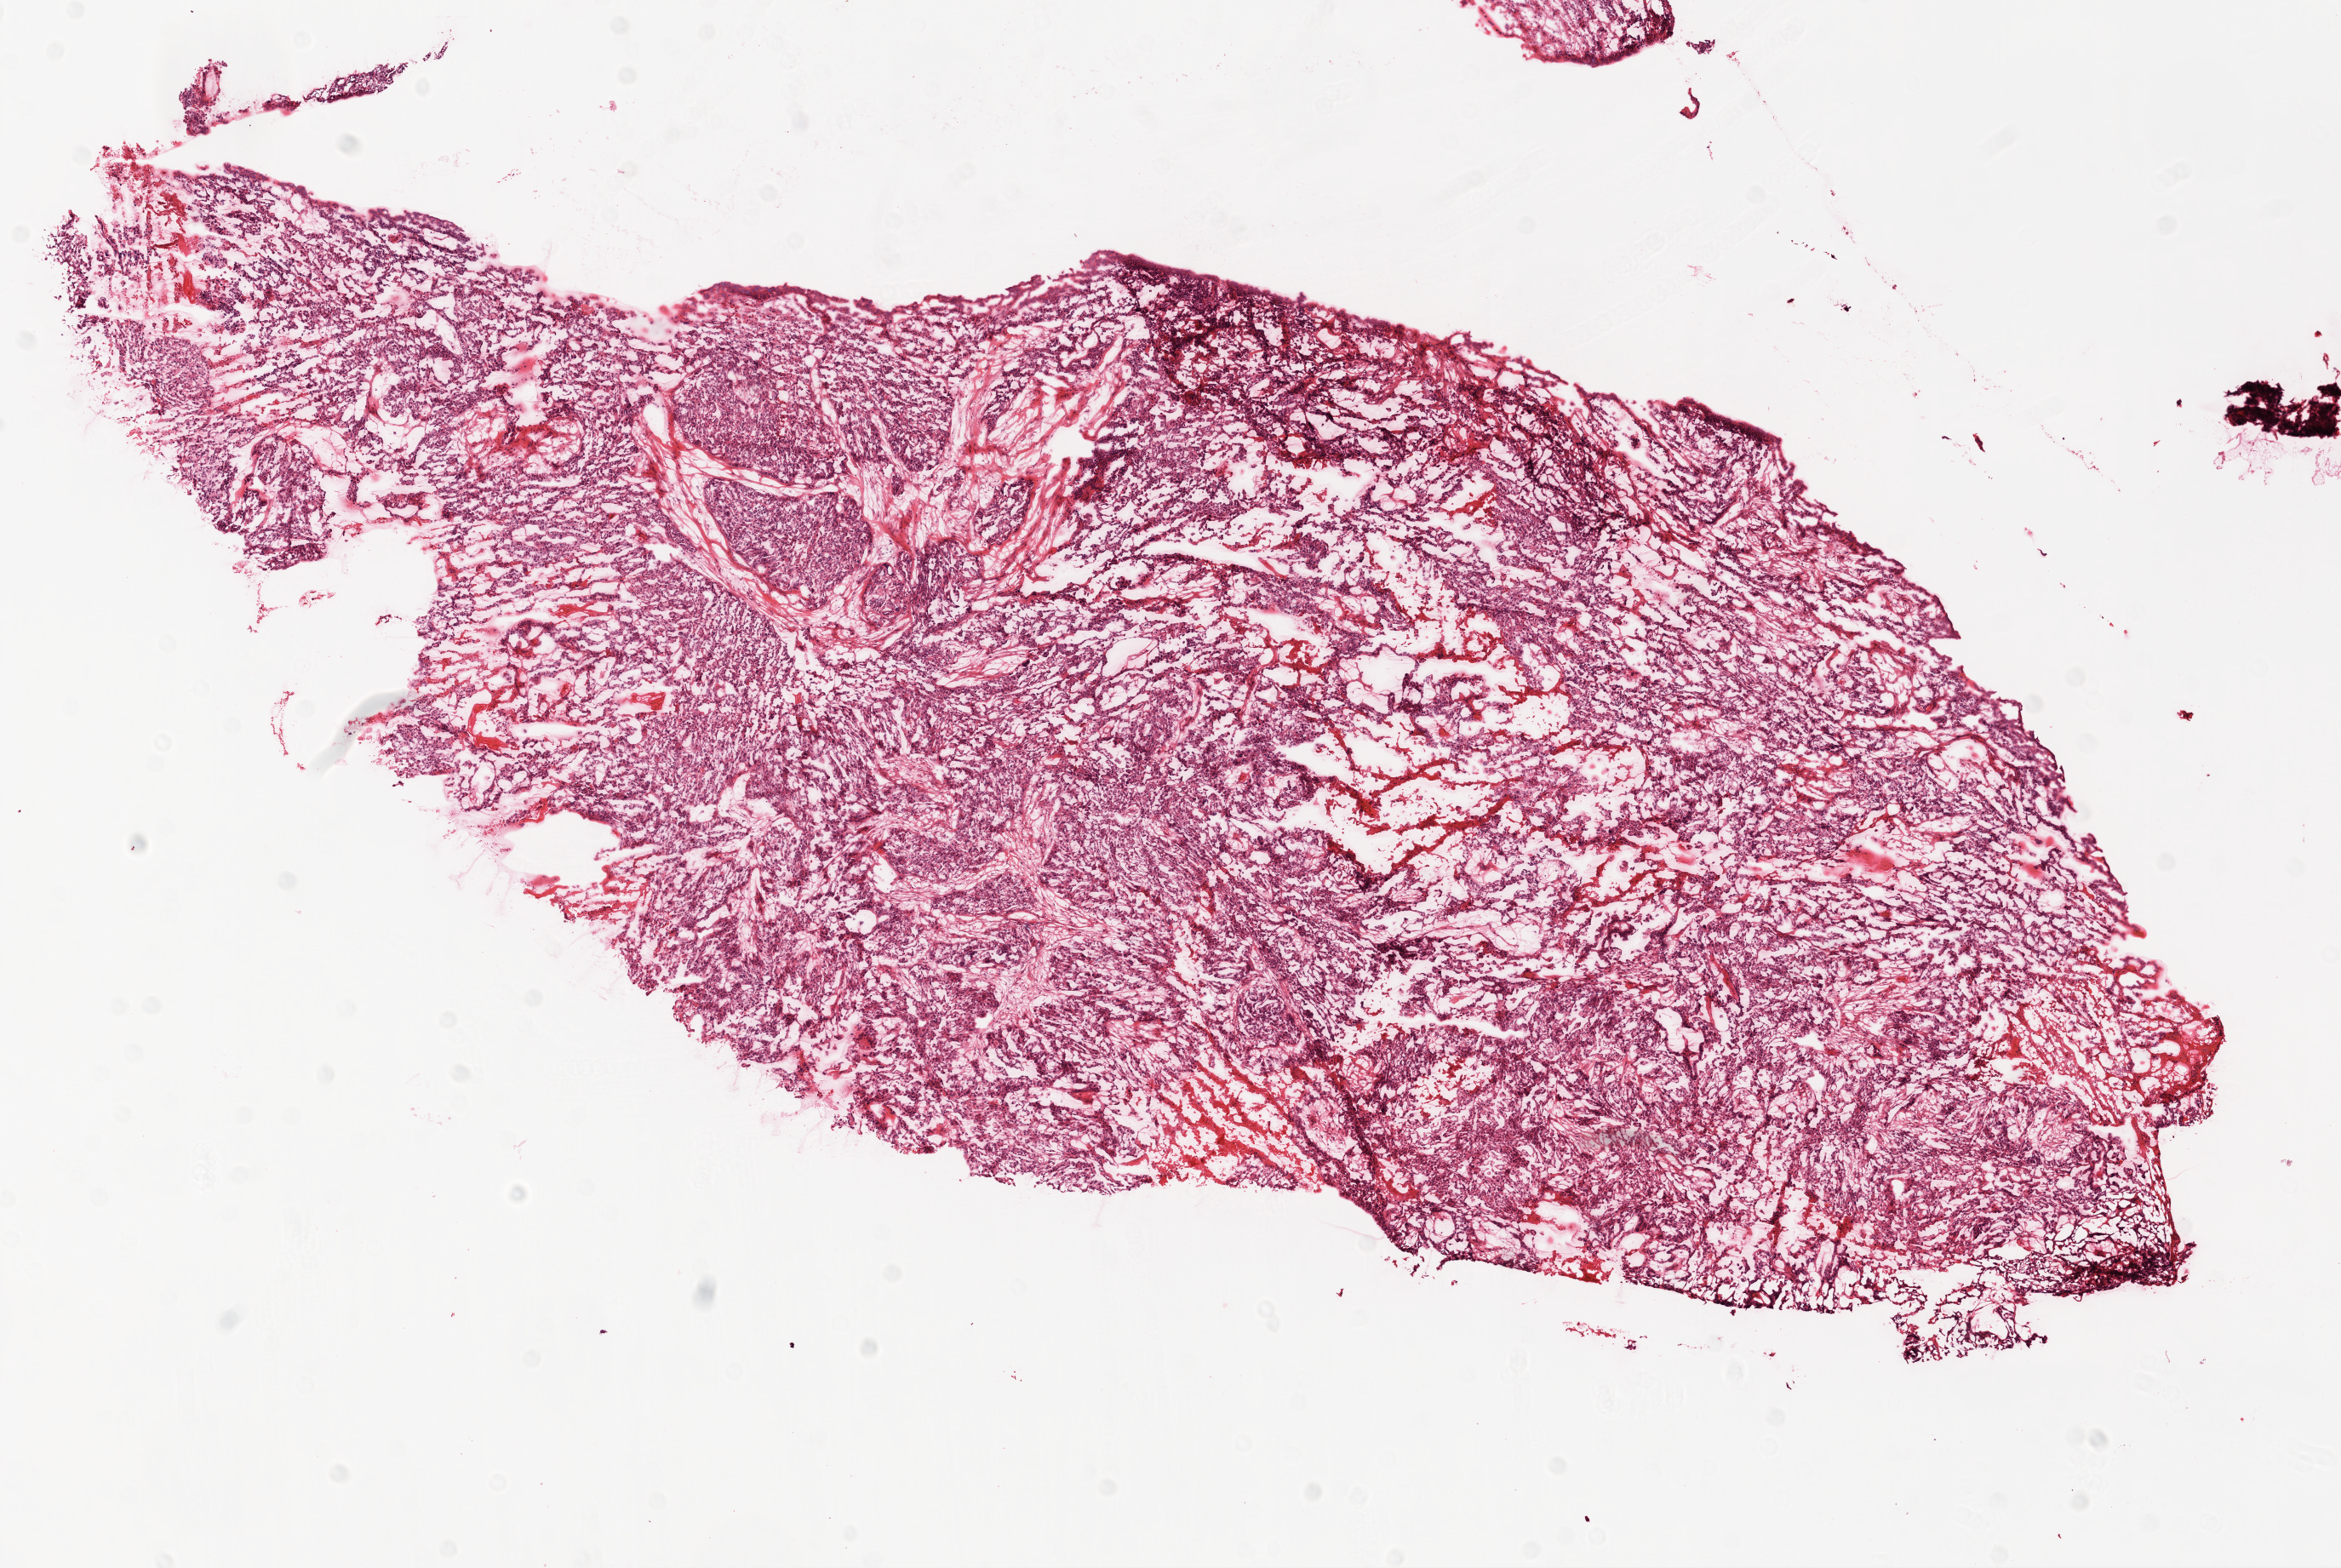
Whole-slide histology image, H&E-stained — low-resolution overview of the scanned area, about 11.0 x 7.4 mm (slide scanned at 20x); frozen section; primary tumour sample from the ovary. Female patient; age at initial diagnosis 53 years. Histologic grade: G2 (moderately differentiated). Slide review estimates, as recorded: tumour cells 80%, tumour nuclei 90%, normal cells 0%, stromal cells 10%, necrosis 10%.
FIGO stage: IIIC. Diagnosis: Serous surface papillary carcinoma.